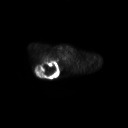
FDG PET of an extremity soft-tissue mass (from a PET/CT study), one axial slice. Slice 210 of 267 in the series (ordered by position). 3.27 mm slice thickness. 128 × 128 image matrix, field of view 700 × 700 mm. Patient: male, 61 years. From the clinical record (not read from this slice): histological type: pleiomorphic spindle cell undifferentiated; grade: high; site of the primary tumour: right parascapusular.
Annotated regions visible in this slice (expert contour drawn on MRI and transferred to this co-registered scan by the dataset authors):
- gross tumour volume including surrounding oedema: bounding box [x1, y1, x2, y2] px = [35, 60, 61, 77]
- gross tumour volume (mass): [36, 60, 58, 76]